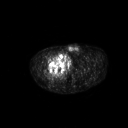
FDG PET of an extremity soft-tissue mass (from a PET/CT study), one axial slice; position 282 of 311 along the scan axis; 3.27 mm slice thickness; 128 × 128 image matrix, field of view 700 × 700 mm. Male patient, age 50 years. From the clinical record (not read from this slice): histological type: undifferentiated - pleiomorphic; grade: high; site of the primary tumour: right thigh.
Structures marked on this image (expert contour drawn on MRI and transferred to this co-registered scan by the dataset authors):
- gross tumour volume including surrounding oedema: bounding box [x1, y1, x2, y2] px = [50, 52, 65, 68]
- gross tumour volume (mass): [50, 53, 65, 68]